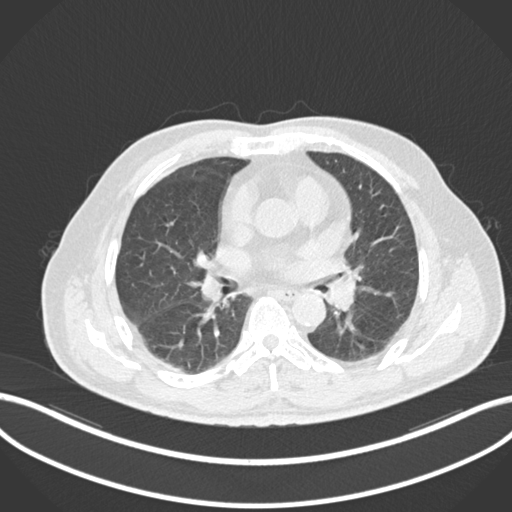
Chest CT, one axial slice; slice 72 of 161 in the series (ordered by position); reconstruction kernel B30f; lung window (W 1500 / L -600 HU); 512 × 512 image matrix, field of view 400 × 400 mm. Patient: male, 71 years. Case-level facts recorded for this patient, not image findings: clinical TNM (as recorded): T1b N0 M0.
Outlined on this slice (rectangle marked by the reading radiologist):
- lung tumour (recorded histology: squamous cell carcinoma): box from (x=320, y=274) to (x=360, y=315) px